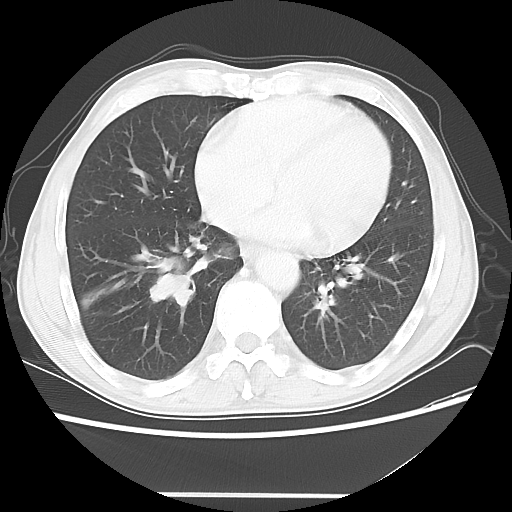
Chest CT, one axial slice. Position 19 of 56 along the scan axis. Reconstruction kernel LUNG. 120 kVp. Lung window (W 1500 / L -600 HU). 512 × 512 image matrix. Male patient, age 65 years. Case-level facts recorded for this patient, not image findings: clinical TNM (as recorded): T1c N3 M0.
Annotated regions visible in this slice (rectangle marked by the reading radiologist):
- lung tumour (recorded histology: small cell carcinoma): bounding box (x1, y1, x2, y2) in pixels: (145, 265, 200, 310)